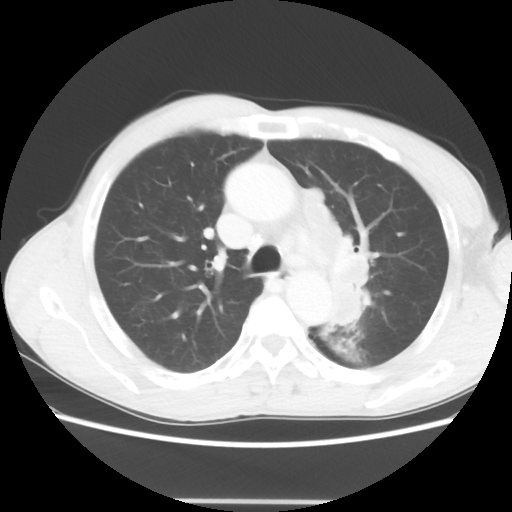
Chest CT, one axial slice; slice 44 of 62 in the series (ordered by position); reconstruction kernel STANDARD; lung window (W 1500 / L -600 HU); 512 × 512 image matrix, field of view 360 × 360 mm. Patient: male, 61 years. From the clinical record (not read from this slice): clinical TNM (as recorded): T3 N1 M1.
Structures marked on this image (rectangle marked by the reading radiologist):
- lung tumour (recorded histology: adenocarcinoma): bounding box [x1, y1, x2, y2] px = [290, 179, 372, 335]